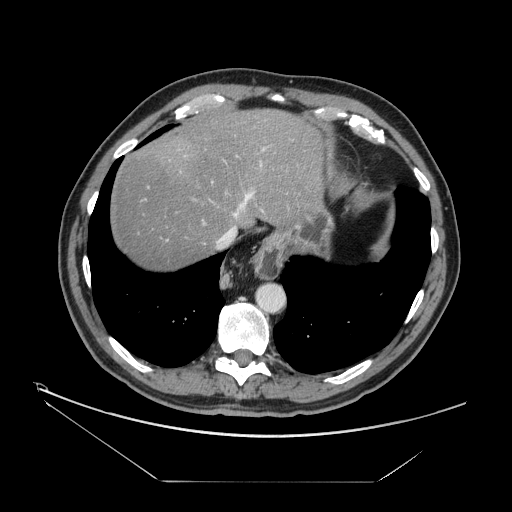
Contrast-enhanced abdominal CT, one axial slice. Position 135 of 161 along the scan axis. Reconstruction kernel STANDARD. Soft-tissue window (W 400 / L 40 HU). 2.5 mm slice thickness. 512 × 512 image matrix, field of view 440 × 440 mm. Male patient, age 65 years. From the clinical record (not read from this slice): diagnosis: colorectal cancer liver metastases, imaged before liver resection; multiple liver metastases: yes; largest metastasis: 4.2 cm; disease in both lobes: yes.
Structures marked on this image (expert manual segmentation):
- hepatic veins: box from (x=204, y=187) to (x=256, y=249) px
- liver: (x=109, y=108)–(x=322, y=269)
- planned liver remnant (the part of the liver to remain after resection): (x=109, y=109)–(x=322, y=269)
- portal vein (with intrahepatic branches): (x=148, y=120)–(x=267, y=241)